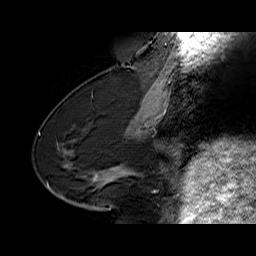
Breast MRI (dynamic contrast-enhanced), one sagittal slice; slice 28 of 60 in the series (ordered by position); dynamic contrast-enhanced series, time point 2 of 6 at this slice position (early post-contrast); 1.5 T; TE 6.4 ms, TR 32.9 ms; 256 × 256 image matrix, field of view 200 × 200 mm. Female patient. Case-level facts recorded for this patient, not image findings: setting: breast cancer imaged before/during neoadjuvant chemotherapy; receptor status: HR-positive, HER2-negative.
Annotated regions visible in this slice (semi-automatic segmentation, software-assisted and operator-edited):
- analysis volume of interest (the breast-tissue region the enhancement analysis was run in; not a lesion): box from (x=68, y=154) to (x=129, y=203) px
- tumour enhancement mask (voxels above the 100 % enhancement threshold inside the analysis volume of interest): (x=92, y=169)–(x=117, y=182)